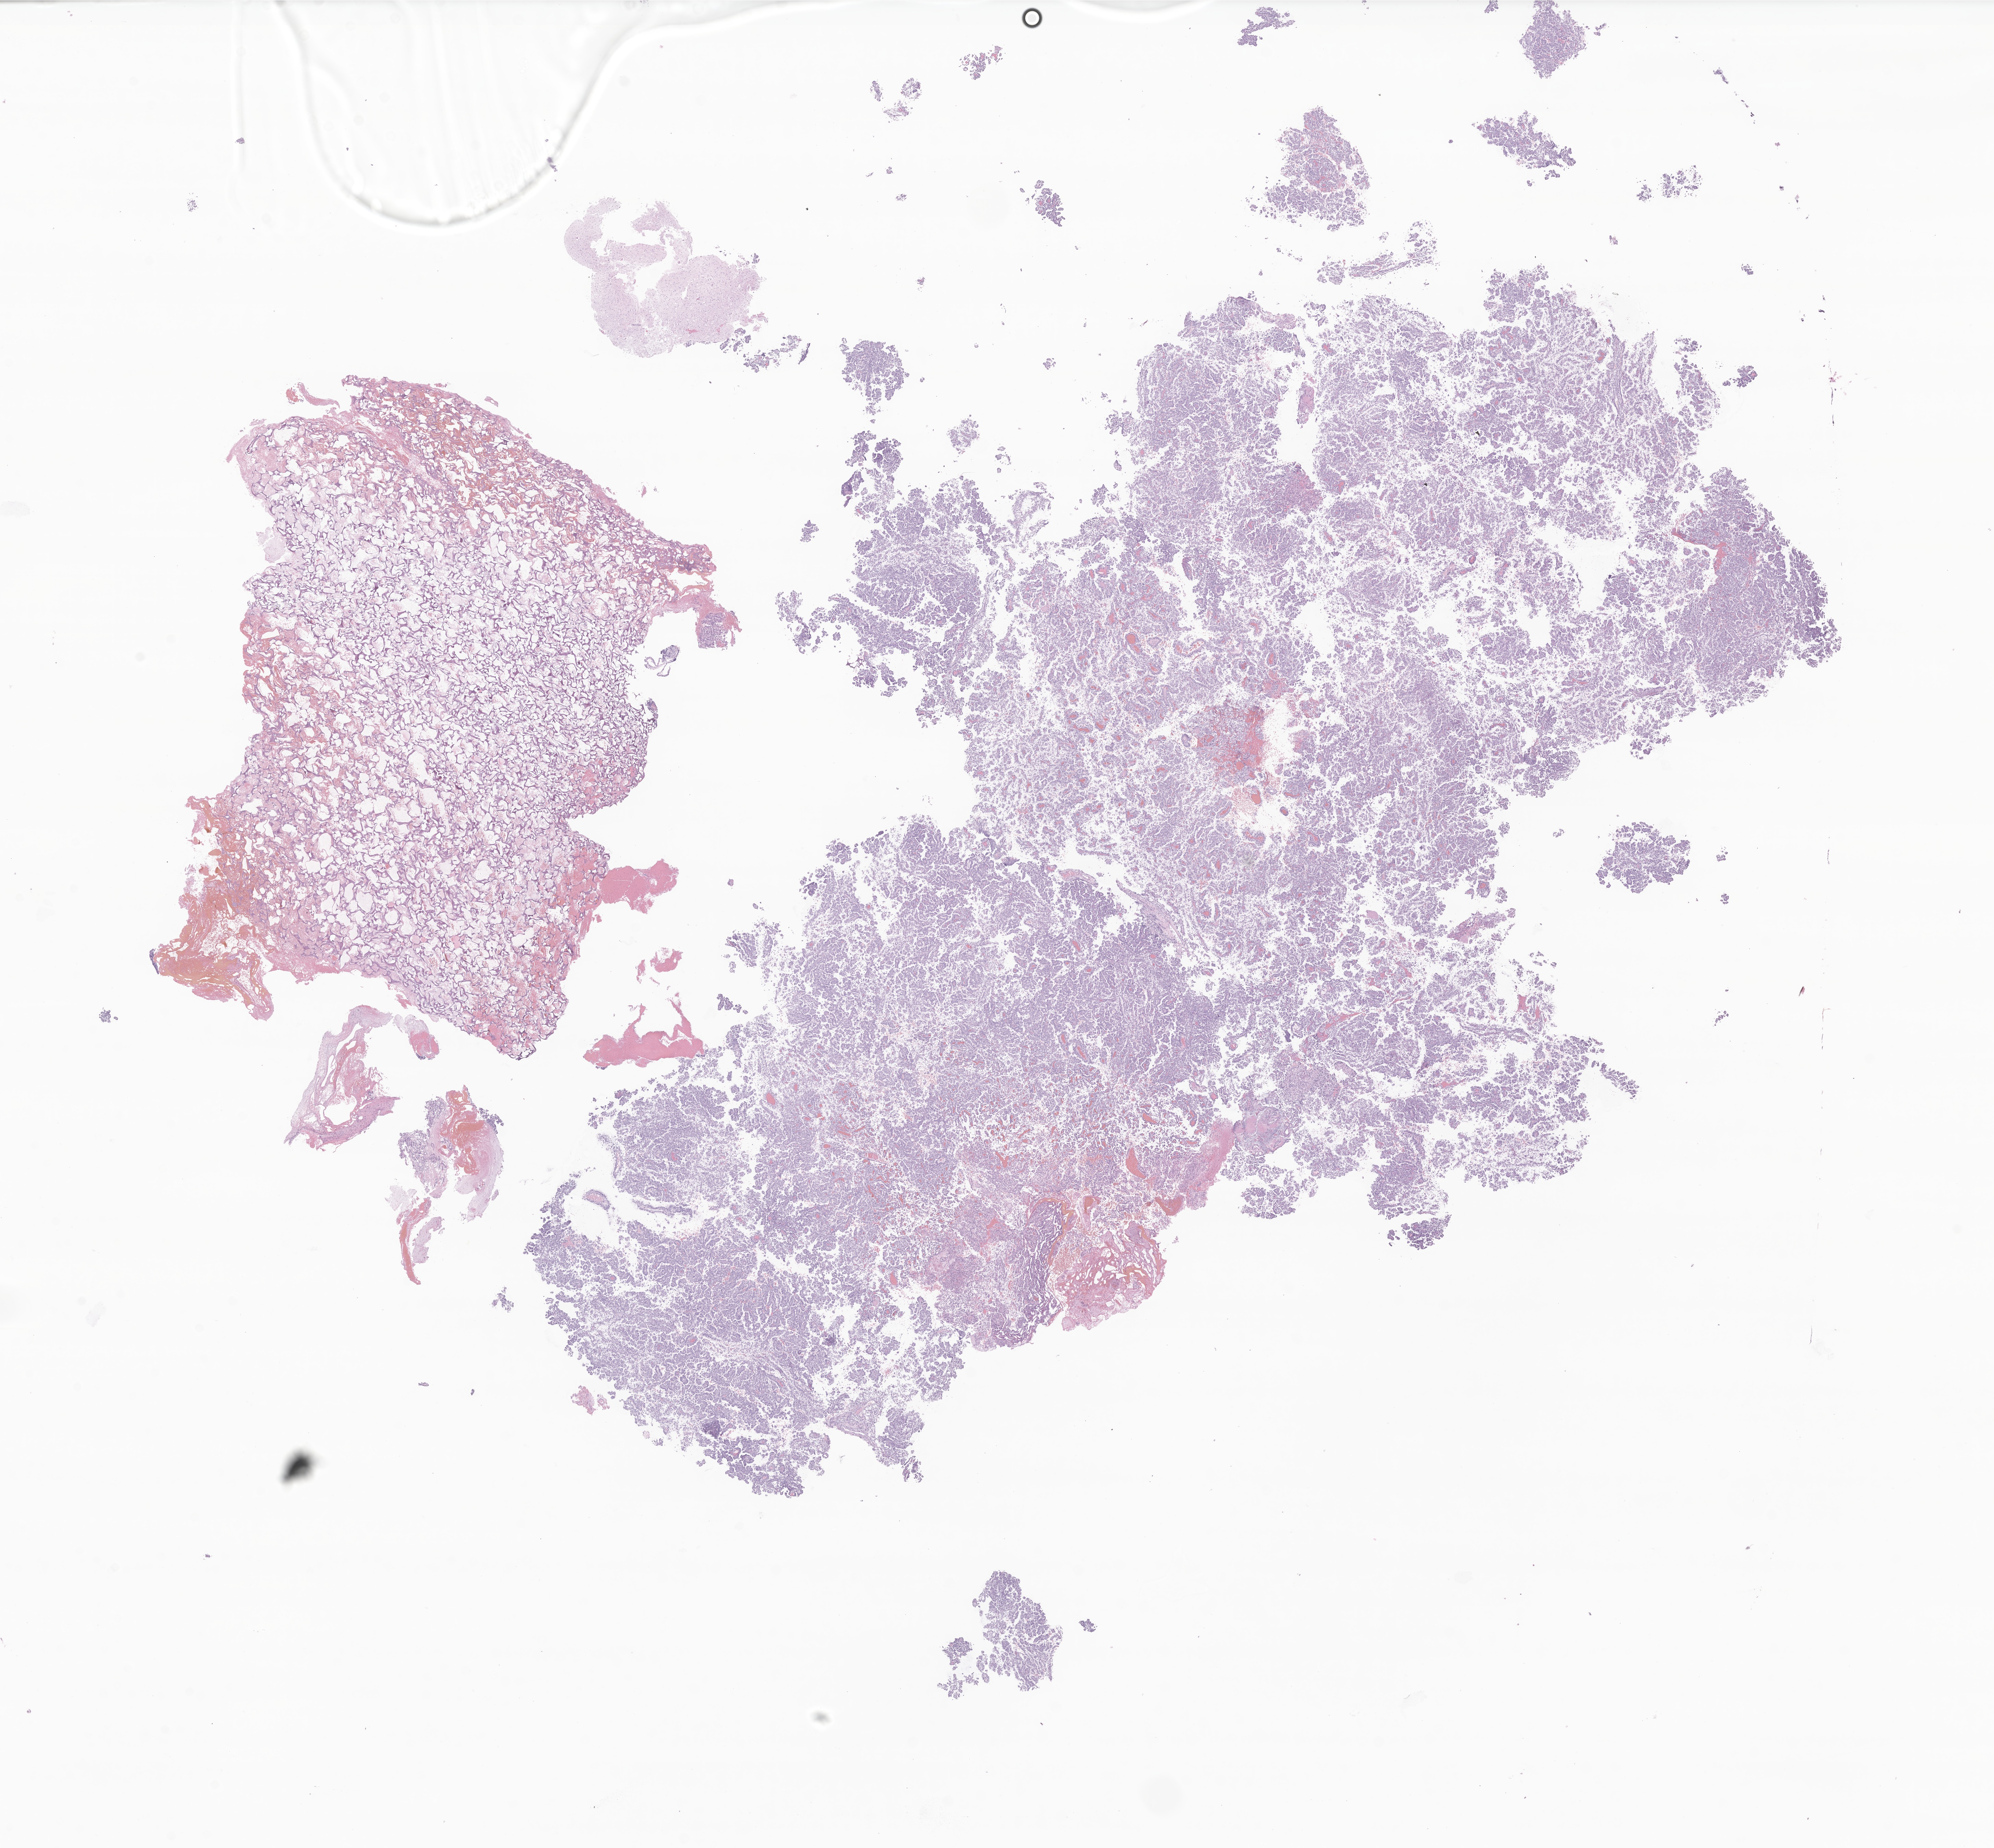
Haematoxylin and eosin whole-slide image of tumor tissue from the brain, a low-resolution overview of the entire scanned area, about 24.5 x 22.7 mm. Formalin-fixed paraffin-embedded section. Patient: male, age 668 days (about 1.8 years).
• recorded diagnosis: Choroid plexus papilloma, NOS